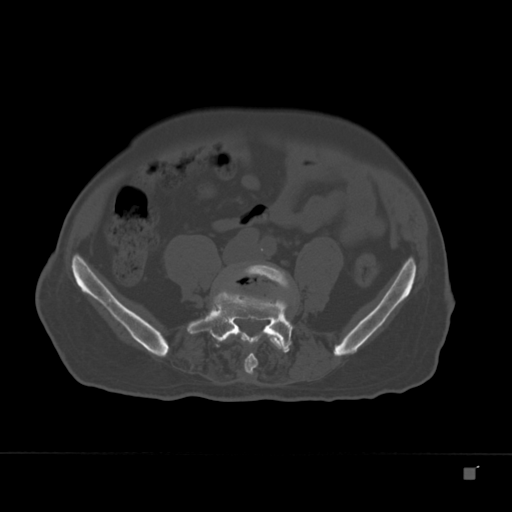
CT including the spine, one axial slice; position 30 of 332 along the scan axis; bone window (W 1800 / L 400 HU); 512 × 512 image matrix, field of view 389 × 389 mm. Male patient, age 72 years. Case-level facts recorded for this patient, not image findings: primary cancer: skeletal.
Outlined on this slice (semi-automatically segmented with operator editing):
- L4 vertebra: box from (x=237, y=264) to (x=292, y=375) px
- L5 vertebra: (x=192, y=282)–(x=292, y=350)